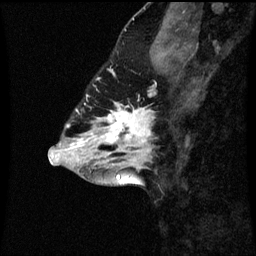
Breast MRI (dynamic contrast-enhanced), one sagittal slice; position 26 of 60 along the scan axis; dynamic contrast-enhanced series, image 2 of 3 at this slice position (ordered by acquisition); 1.5 T; TE 4.2 ms, TR 8.9 ms; 2 mm slice thickness; 256 × 256 image matrix, field of view 200 × 200 mm. Patient: female, 43 years. From the clinical record (not read from this slice): setting: breast cancer imaged before/during neoadjuvant chemotherapy; receptor status: HR-positive, HER2-negative.
Outlined on this slice (semi-automatically segmented with operator editing):
- analysis volume of interest (the breast-tissue region the enhancement analysis was run in; not a lesion): bounding box <96,96,155,159> (left, top, right, bottom; pixels)
- tumour enhancement mask (voxels above the 70 % enhancement threshold inside the analysis volume of interest): <106,96,153,149>